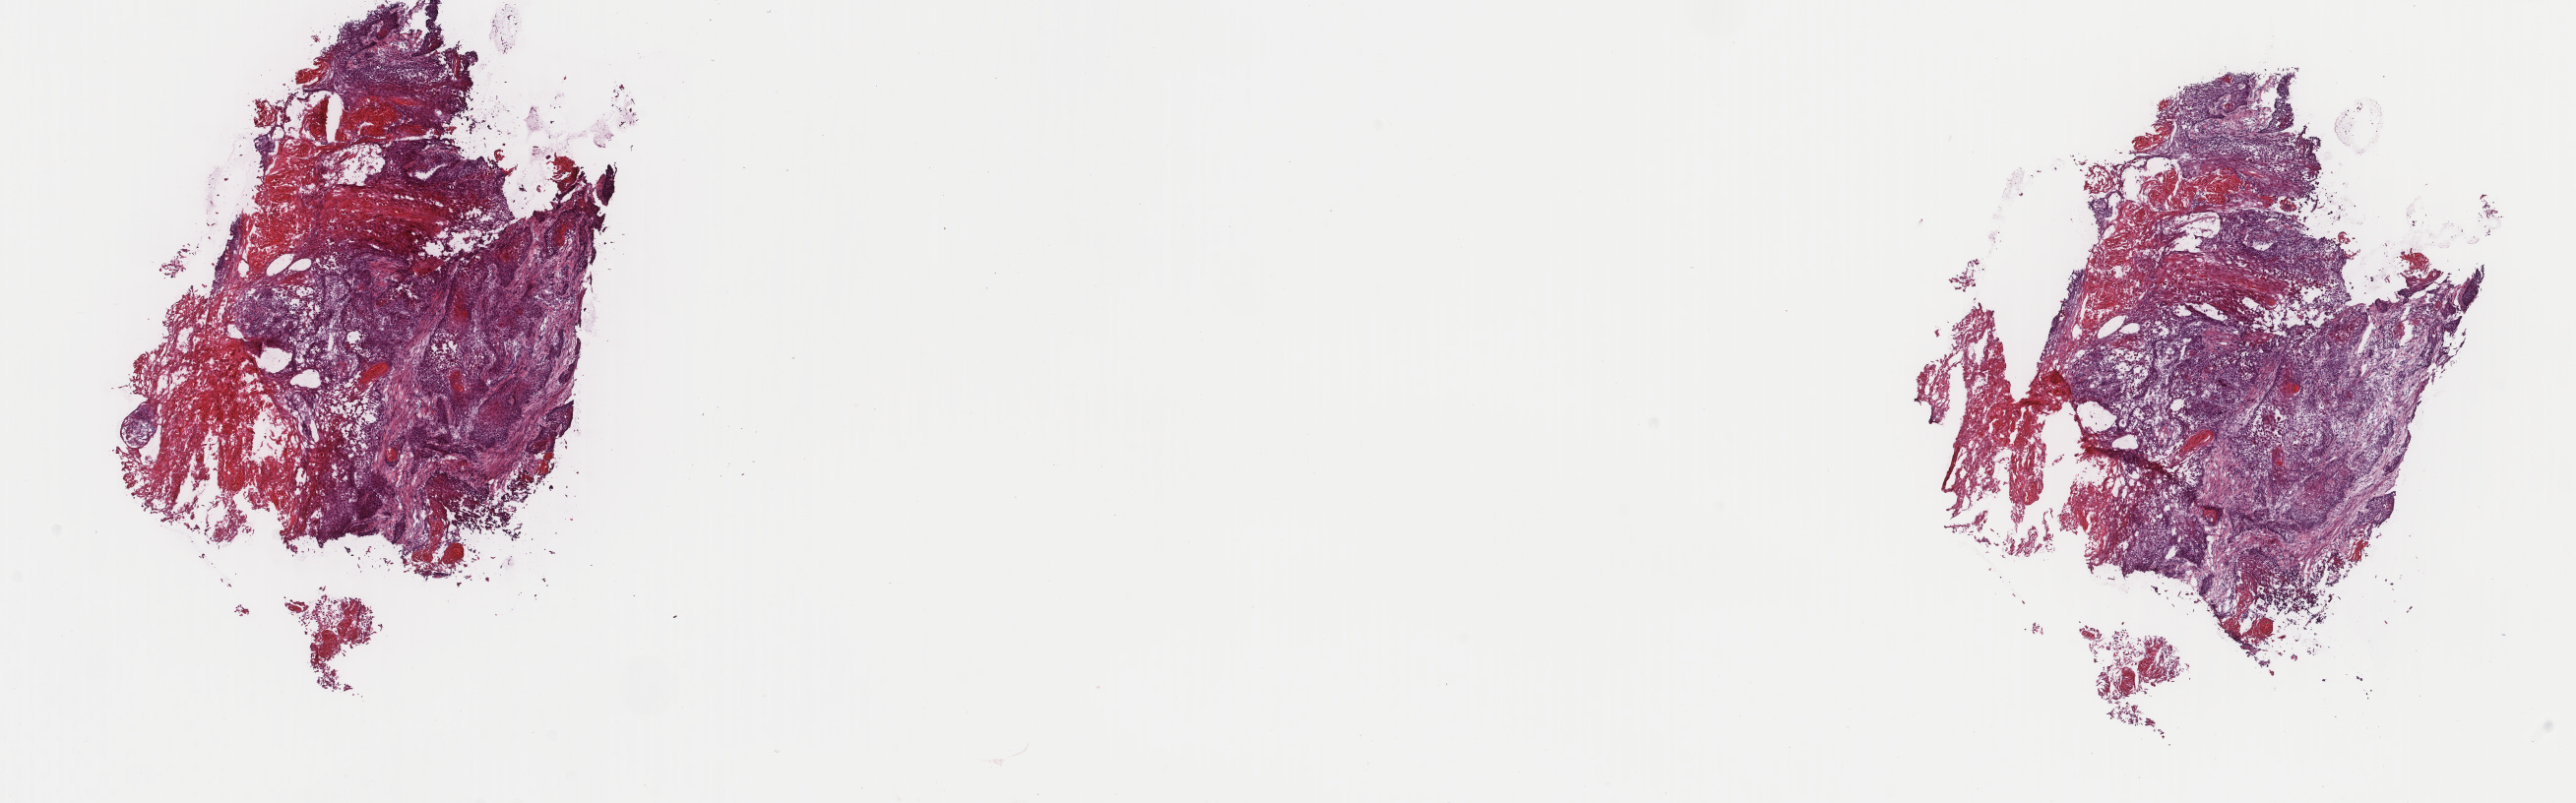
Whole-slide histology image, Hematoxylin and eosin (H&E) stained — shown as a low-resolution overview of the whole scanned area (about 20.8 x 6.5 mm, acquisition: 40x scan). Frozen section from the top of the tissue portion. Sample: primary tumour, esophagus. Male patient; age at initial diagnosis 62 years. Histologic grade: G1 (well differentiated). Pathologist review of this section (percent, as recorded): tumour cells 100%, tumour nuclei 85%, normal cells 0%, stromal cells 0%, necrosis 0%. Inflammatory infiltration, as recorded: lymphocyte infiltration 0%, monocyte infiltration 0%, neutrophil infiltration 0%.
* AJCC pathologic stage: IIA (6th edition)
* TNM: T2 N0 M0
* pathologic diagnosis: Squamous cell carcinoma, NOS